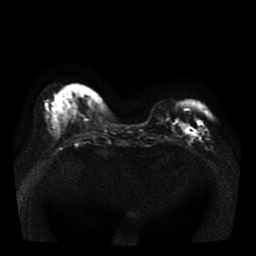
Breast MRI, one axial slice. Position 14 of 41 along the scan axis. Diffusion-weighted series; image 2 of 4 stored at this slice position (different b-values; order by instance number). 1.5 T. 256 × 256 image matrix. Female patient.
Annotated regions visible in this slice (outlined manually by an expert reader):
- tumour on diffusion-weighted imaging: bounding box (x1, y1, x2, y2) in pixels: (185, 127, 197, 137)